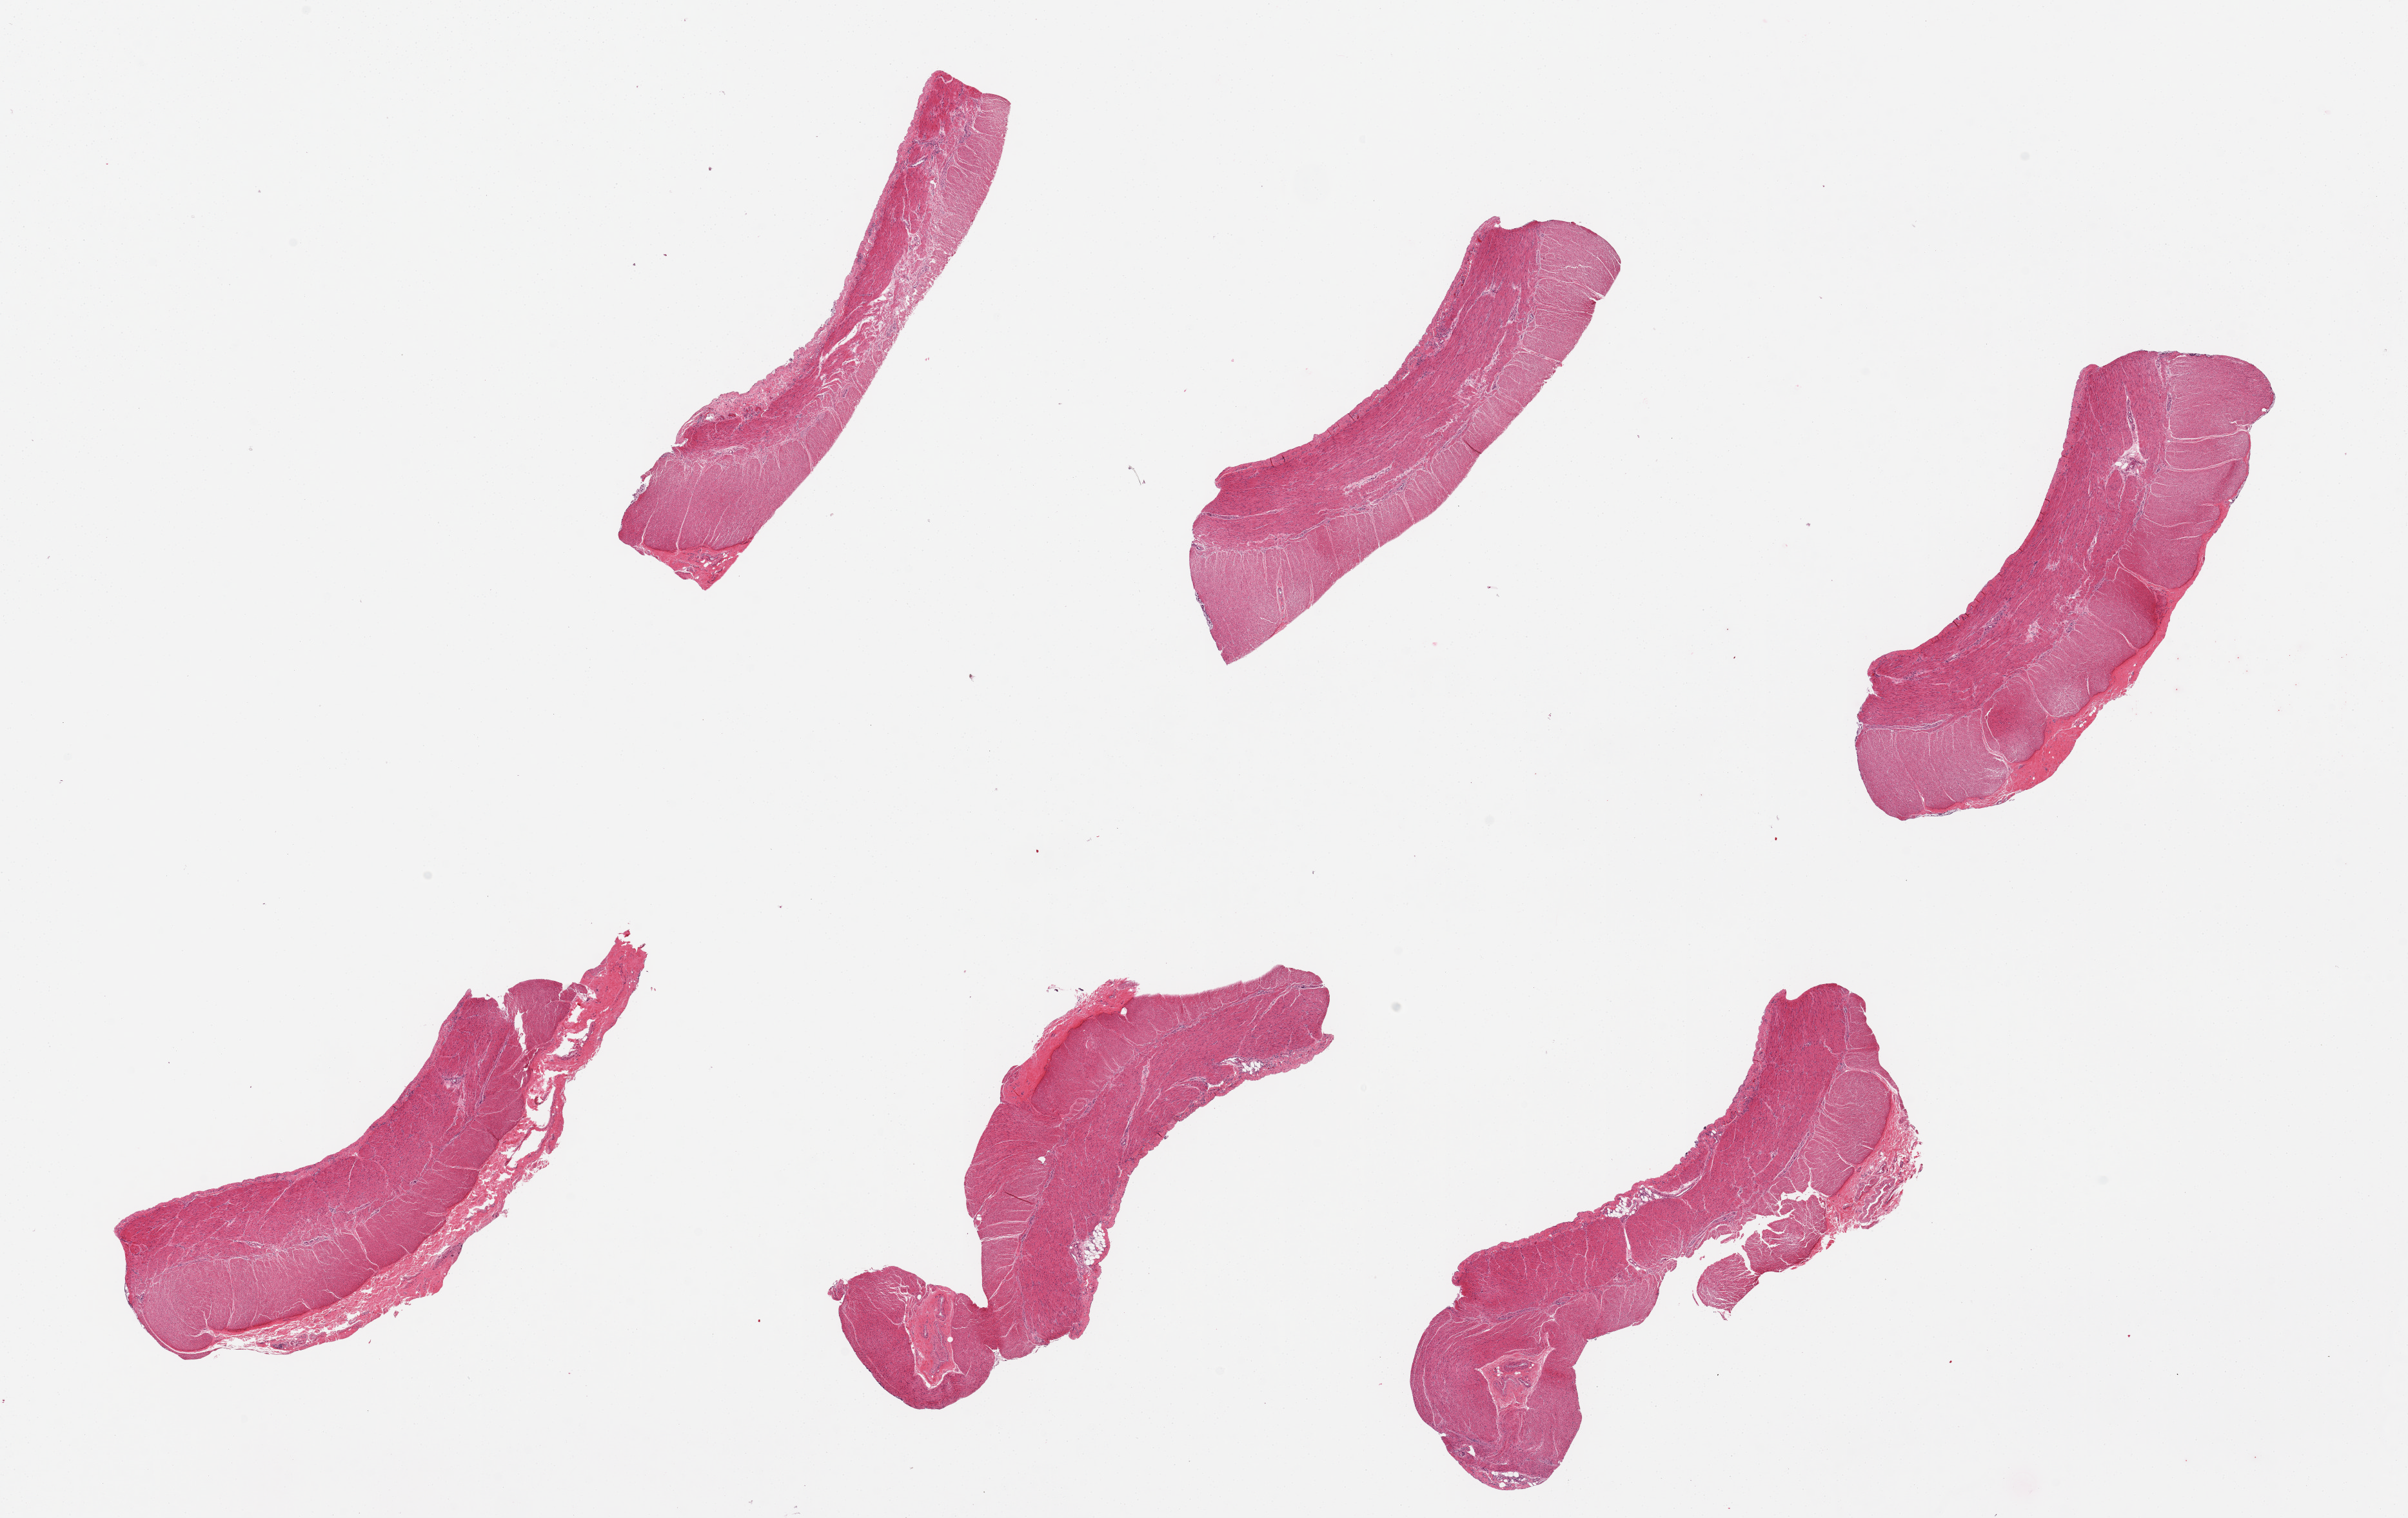
Whole-slide image, haematoxylin and eosin stain — low-resolution overview of the scanned area, about 29.5 x 18.6 mm, PAXgene-fixed paraffin-embedded (PFPE) section, sampled site (target tissue): sigmoid colon, tissue donor sample. Donor sex: male.
Reviewer comment on this tissue sample: 6 pieces. Well trimmed muscle.